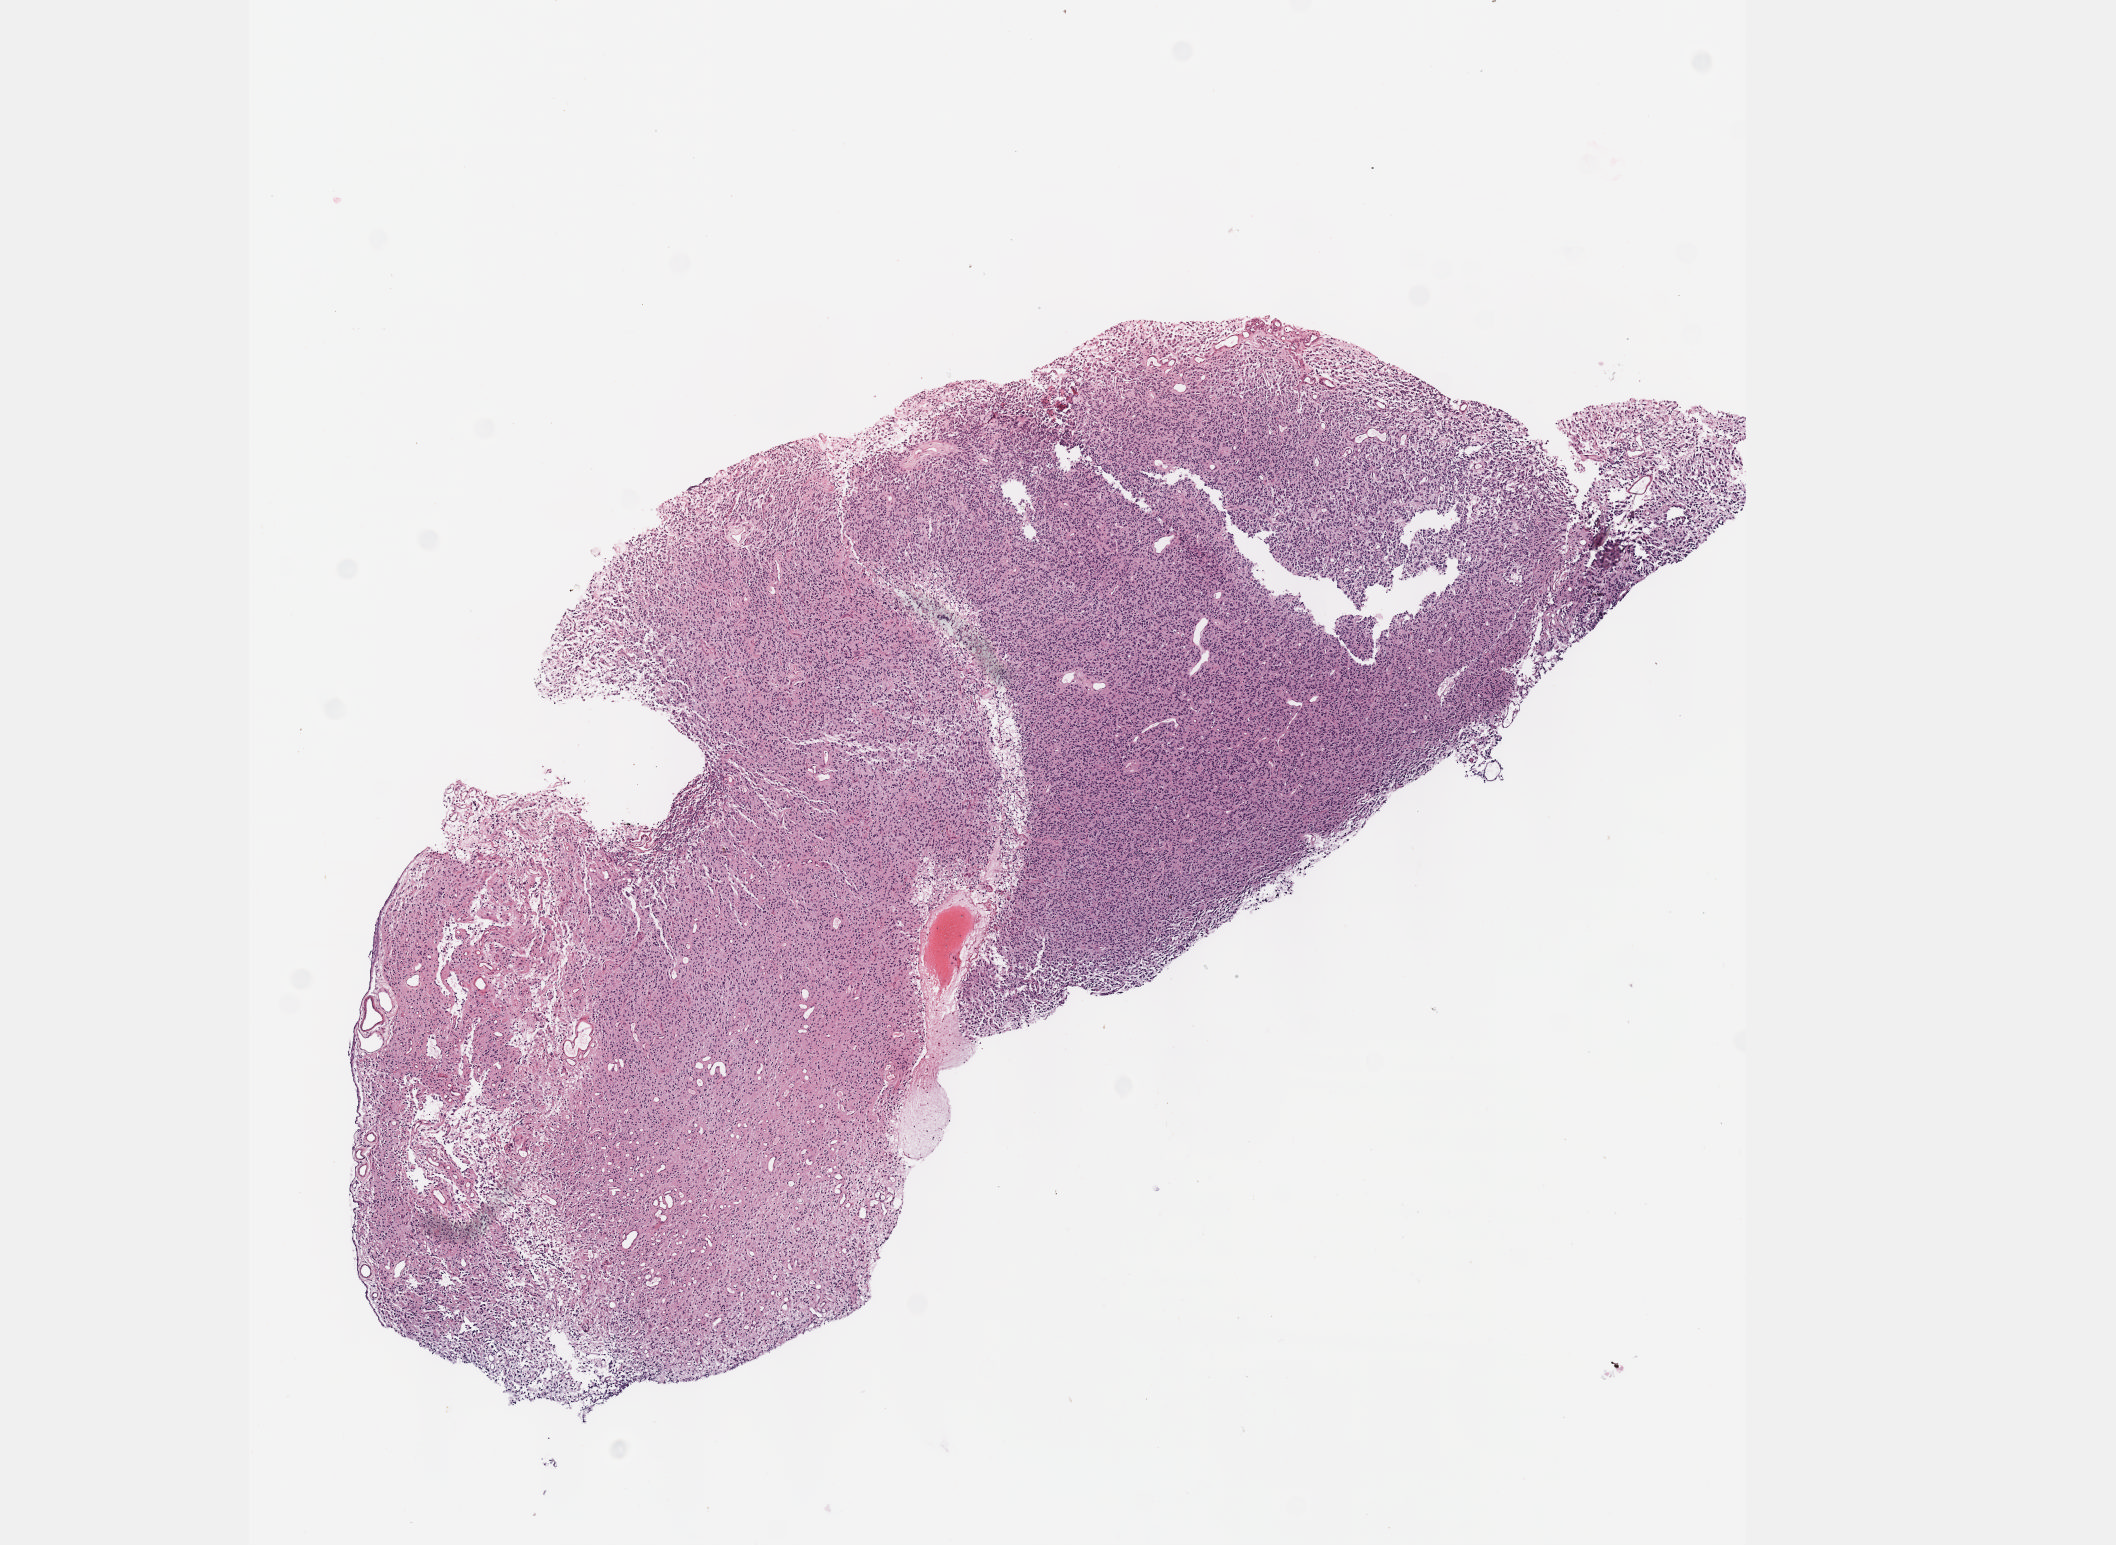
Digitized H&E-stained tissue section (whole slide) — a low-resolution overview of the entire scanned area, about 8.6 x 6.2 mm (from a 40x scan). Formalin-fixed paraffin-embedded (FFPE) diagnostic section. Sample: primary tumour, brain. Female patient; age at initial diagnosis 57 years. Histologic grade: G3 (poorly differentiated).
• histologic diagnosis: Oligodendroglioma, anaplastic (cerebrum)